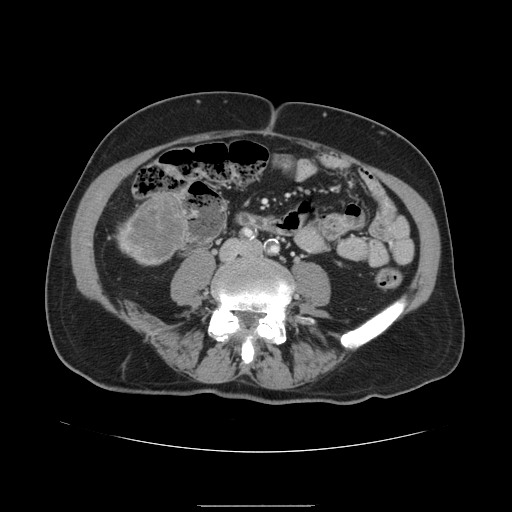
Contrast-enhanced abdominal CT, one axial slice. Slice 13 of 168 in the series (ordered by position). 120 kVp. Intravenous contrast given. Soft-tissue window (W 400 / L 40 HU). 2.5 mm slice thickness. 512 × 512 image matrix, field of view 386 × 386 mm. Male patient, age 74 years. From the clinical record (not read from this slice): diagnosis: colorectal cancer liver metastases, imaged before liver resection; multiple liver metastases: no; largest metastasis: 14.5 cm; disease in both lobes: yes.
Annotated regions visible in this slice (expert manual segmentation):
- liver: box from (x=119, y=191) to (x=190, y=266) px
- liver metastasis: (x=124, y=194)–(x=187, y=262)